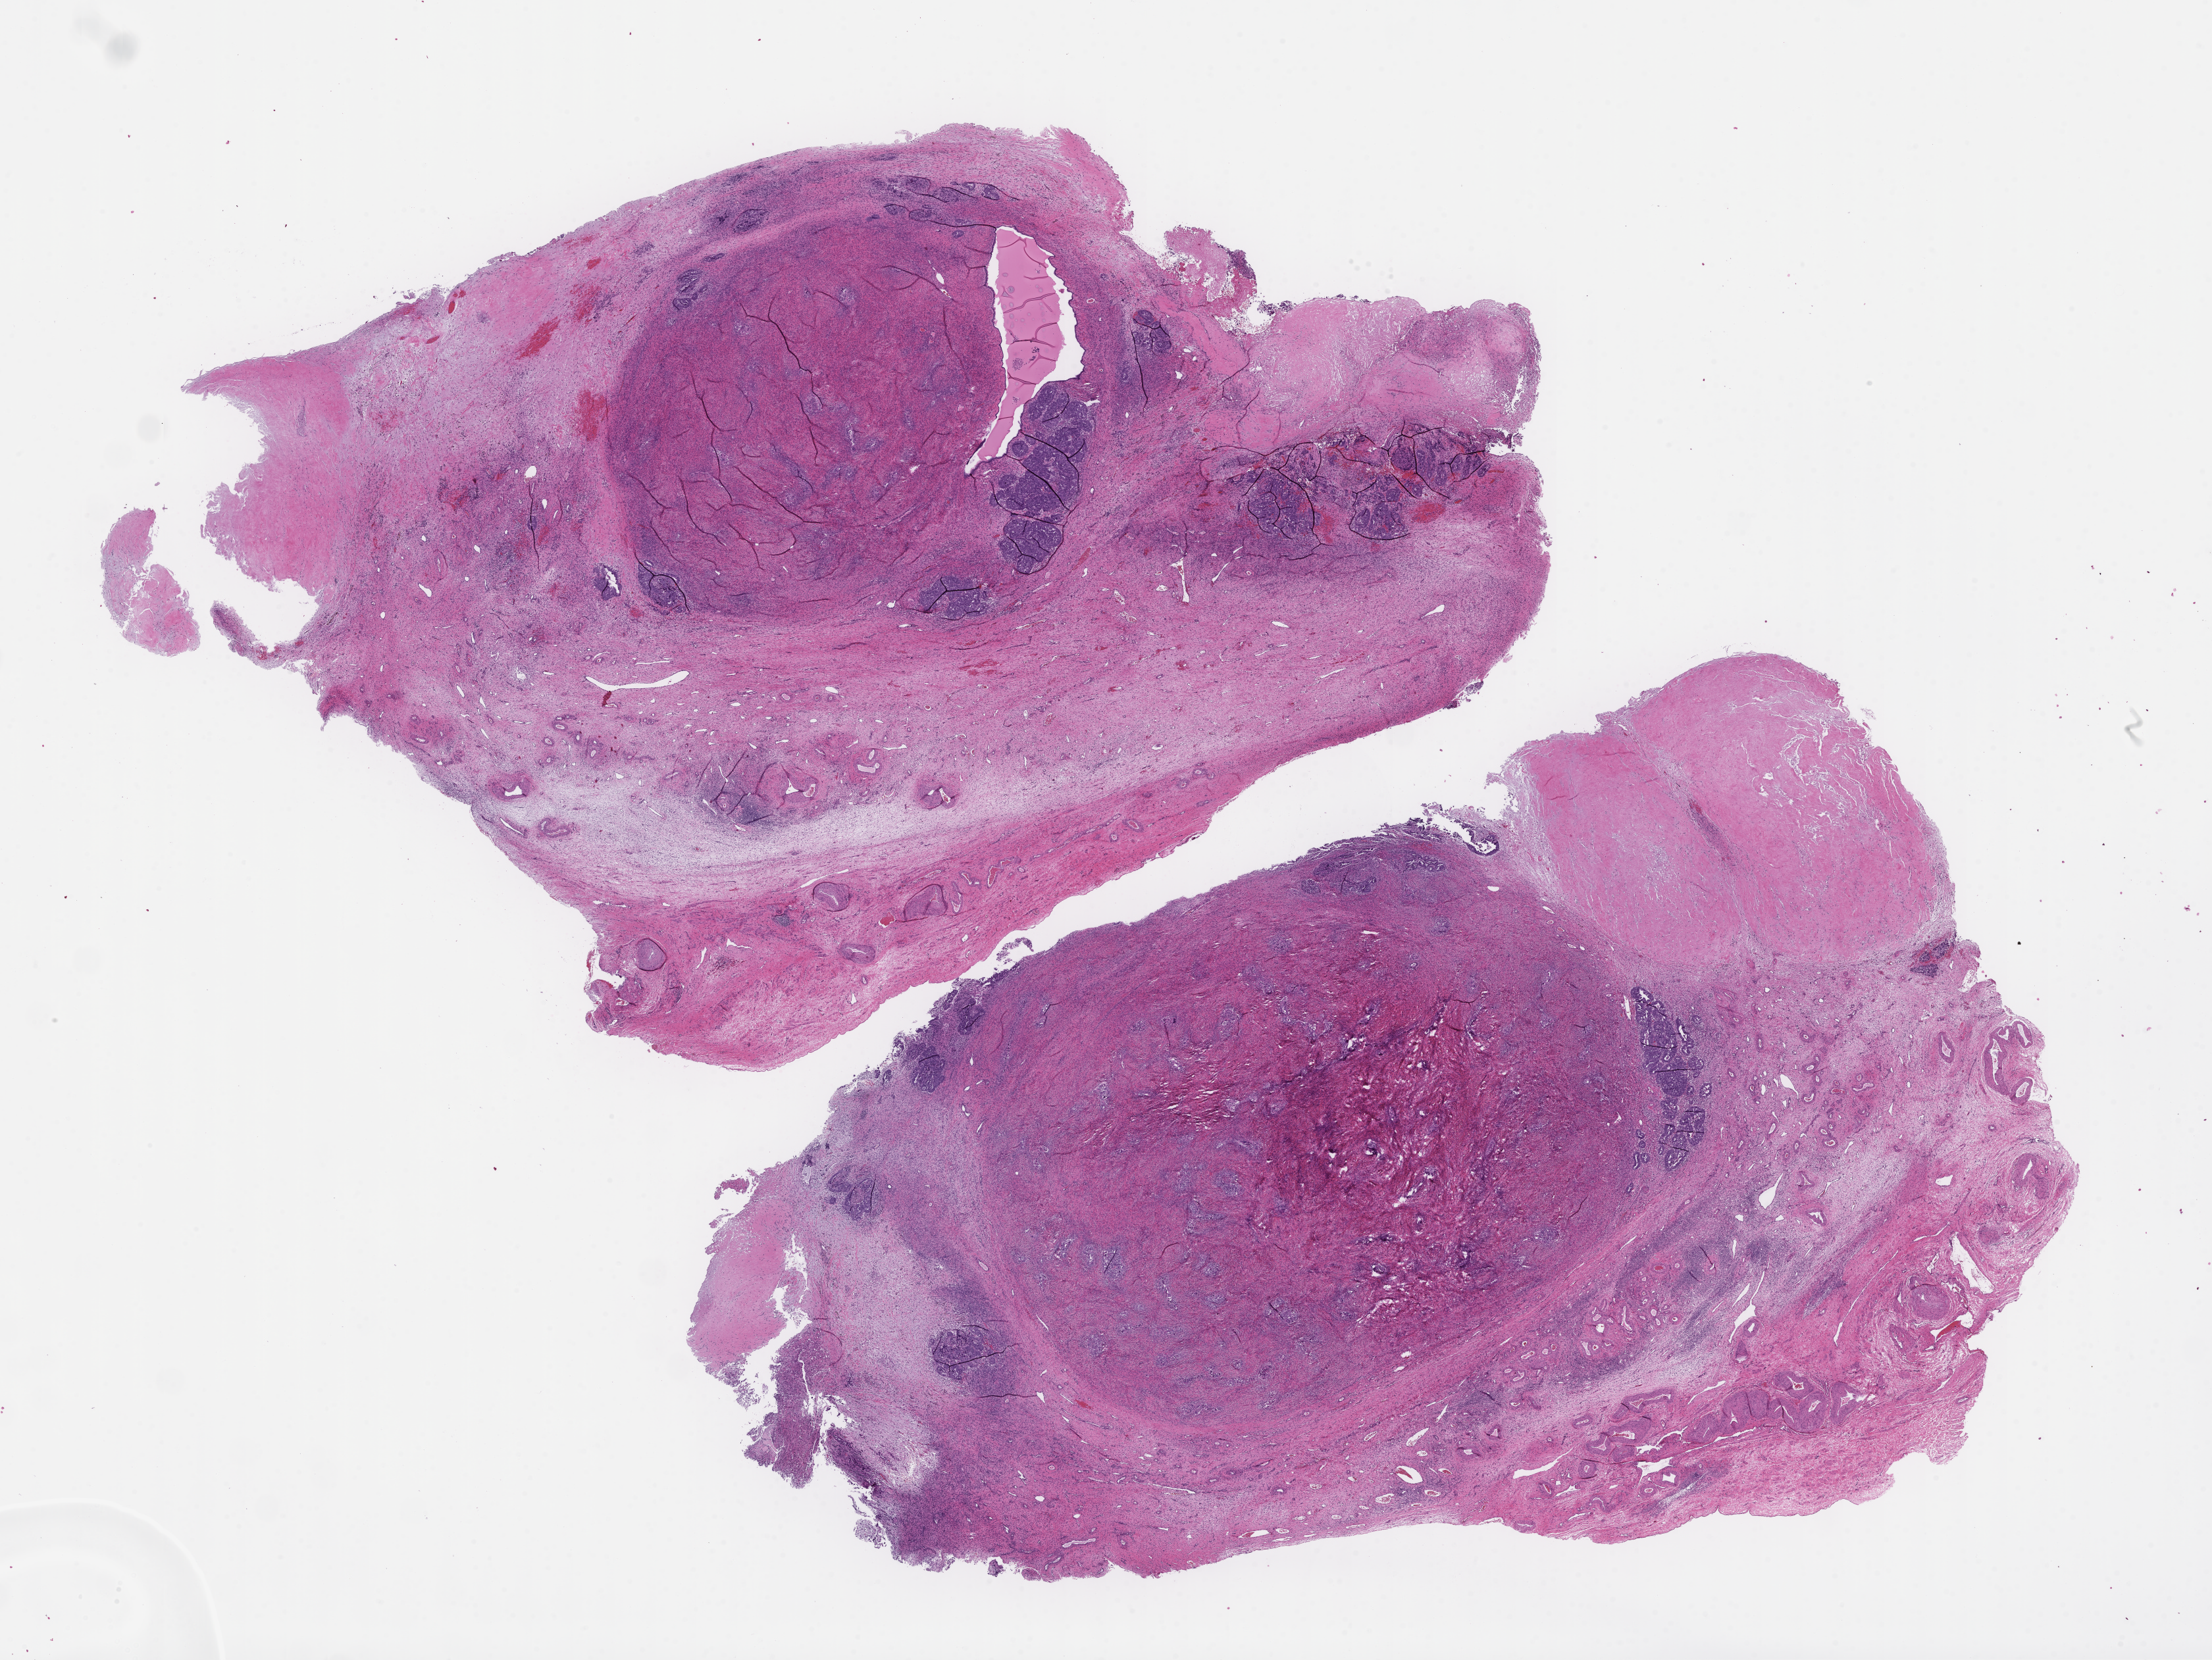
Whole-slide image, hematoxylin and eosin (H&E) stain — whole scanned area (about 27.1 x 20.4 mm) shown as a low-resolution overview, formalin-fixed, paraffin-embedded (FFPE) tissue, tissue site: ovary. Patient sex: female.
This section: primary tumor. Diagnosis: Ovarian Carcinoma.